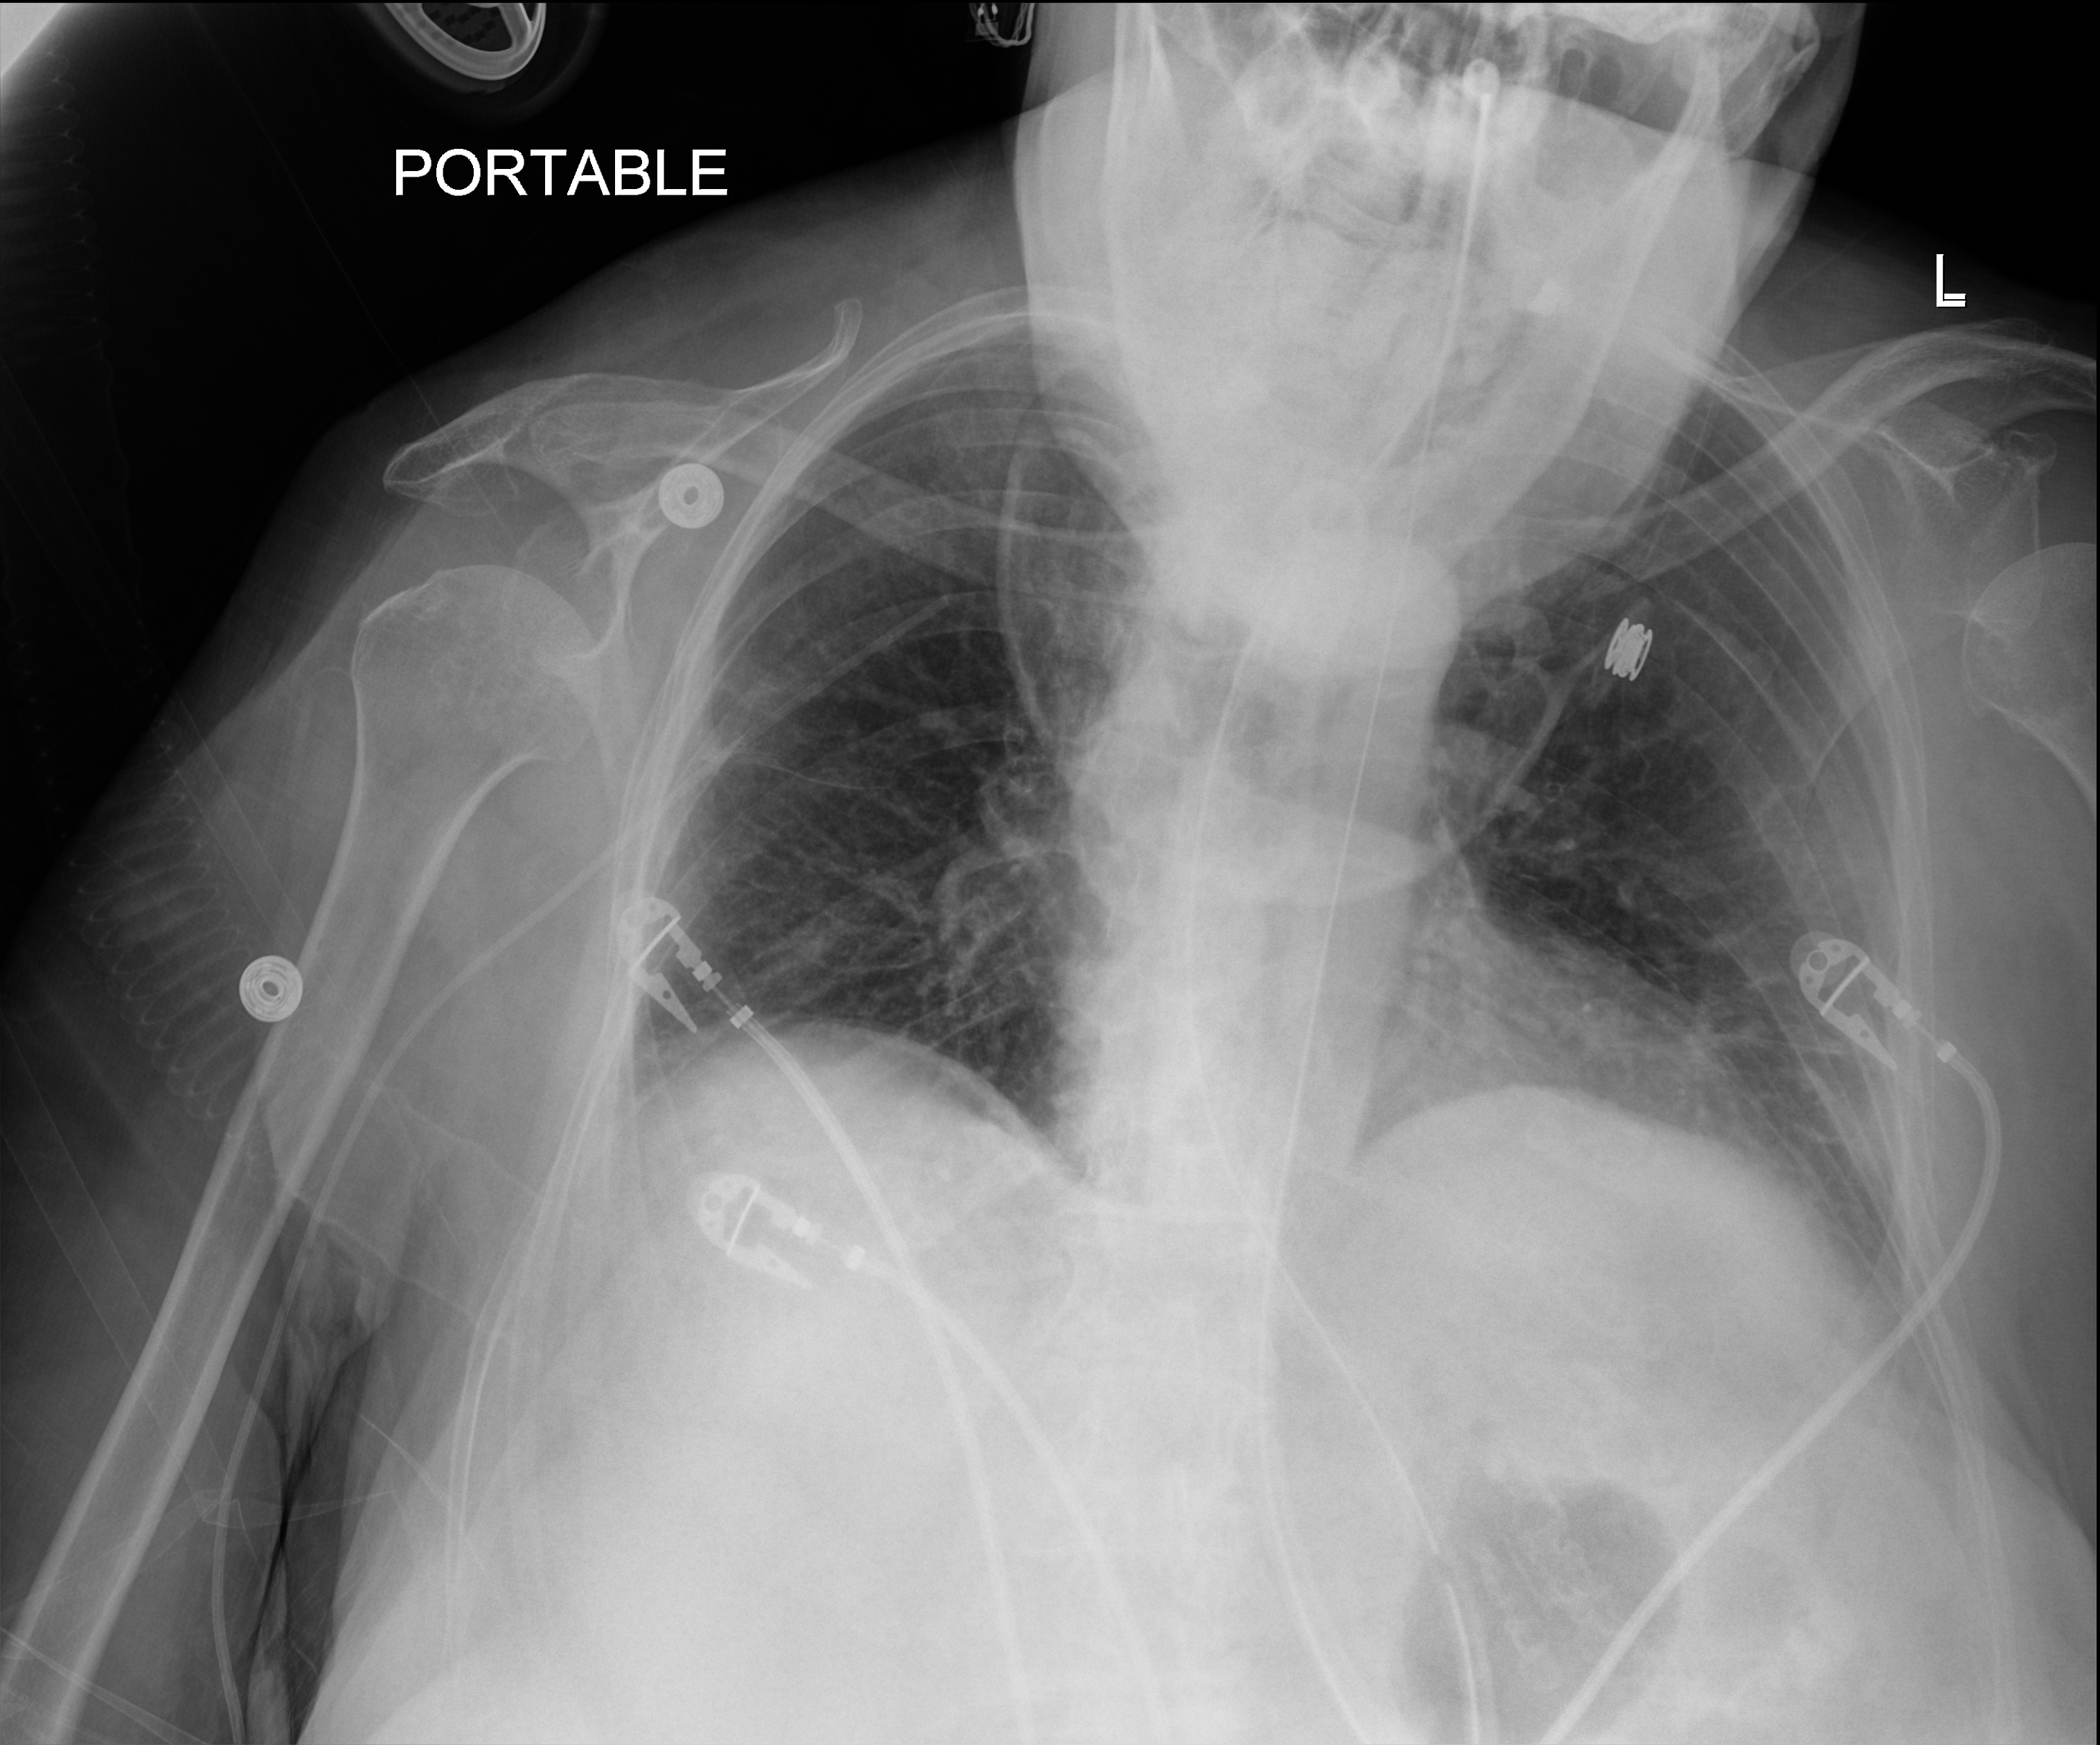
Portable chest radiograph; anteroposterior (AP) projection. Patient hospitalised with COVID-19; female, aged 75–90 years.
From the hospital-stay record, not from the radiograph (when in the stay this image was taken is not recorded):
- length of hospital stay: 82 days
- admitted to intensive care during this hospital stay: yes
- hypertension (admission record): yes